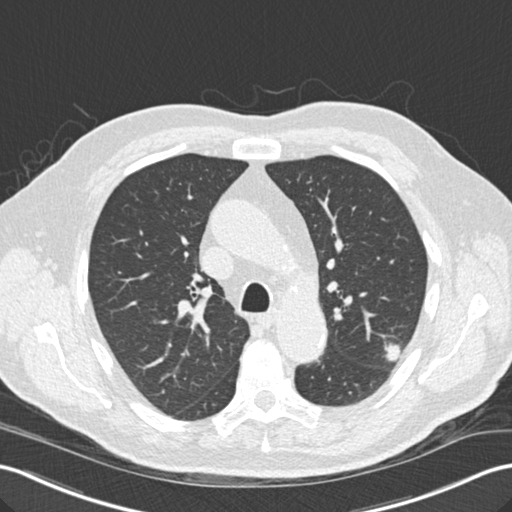
Low-dose screening chest CT, one axial slice; position 103 of 157 along the scan axis; reconstruction kernel B30f; 120 kVp; lung window (W 1500 / L -600 HU); 2 mm slice thickness; 512 × 512 image matrix.
Annotated regions visible in this slice (expert manual segmentation):
- lesion 1 (tumor, upper lobe of left lung): bounding box [x1, y1, x2, y2] px = [385, 344, 401, 361]